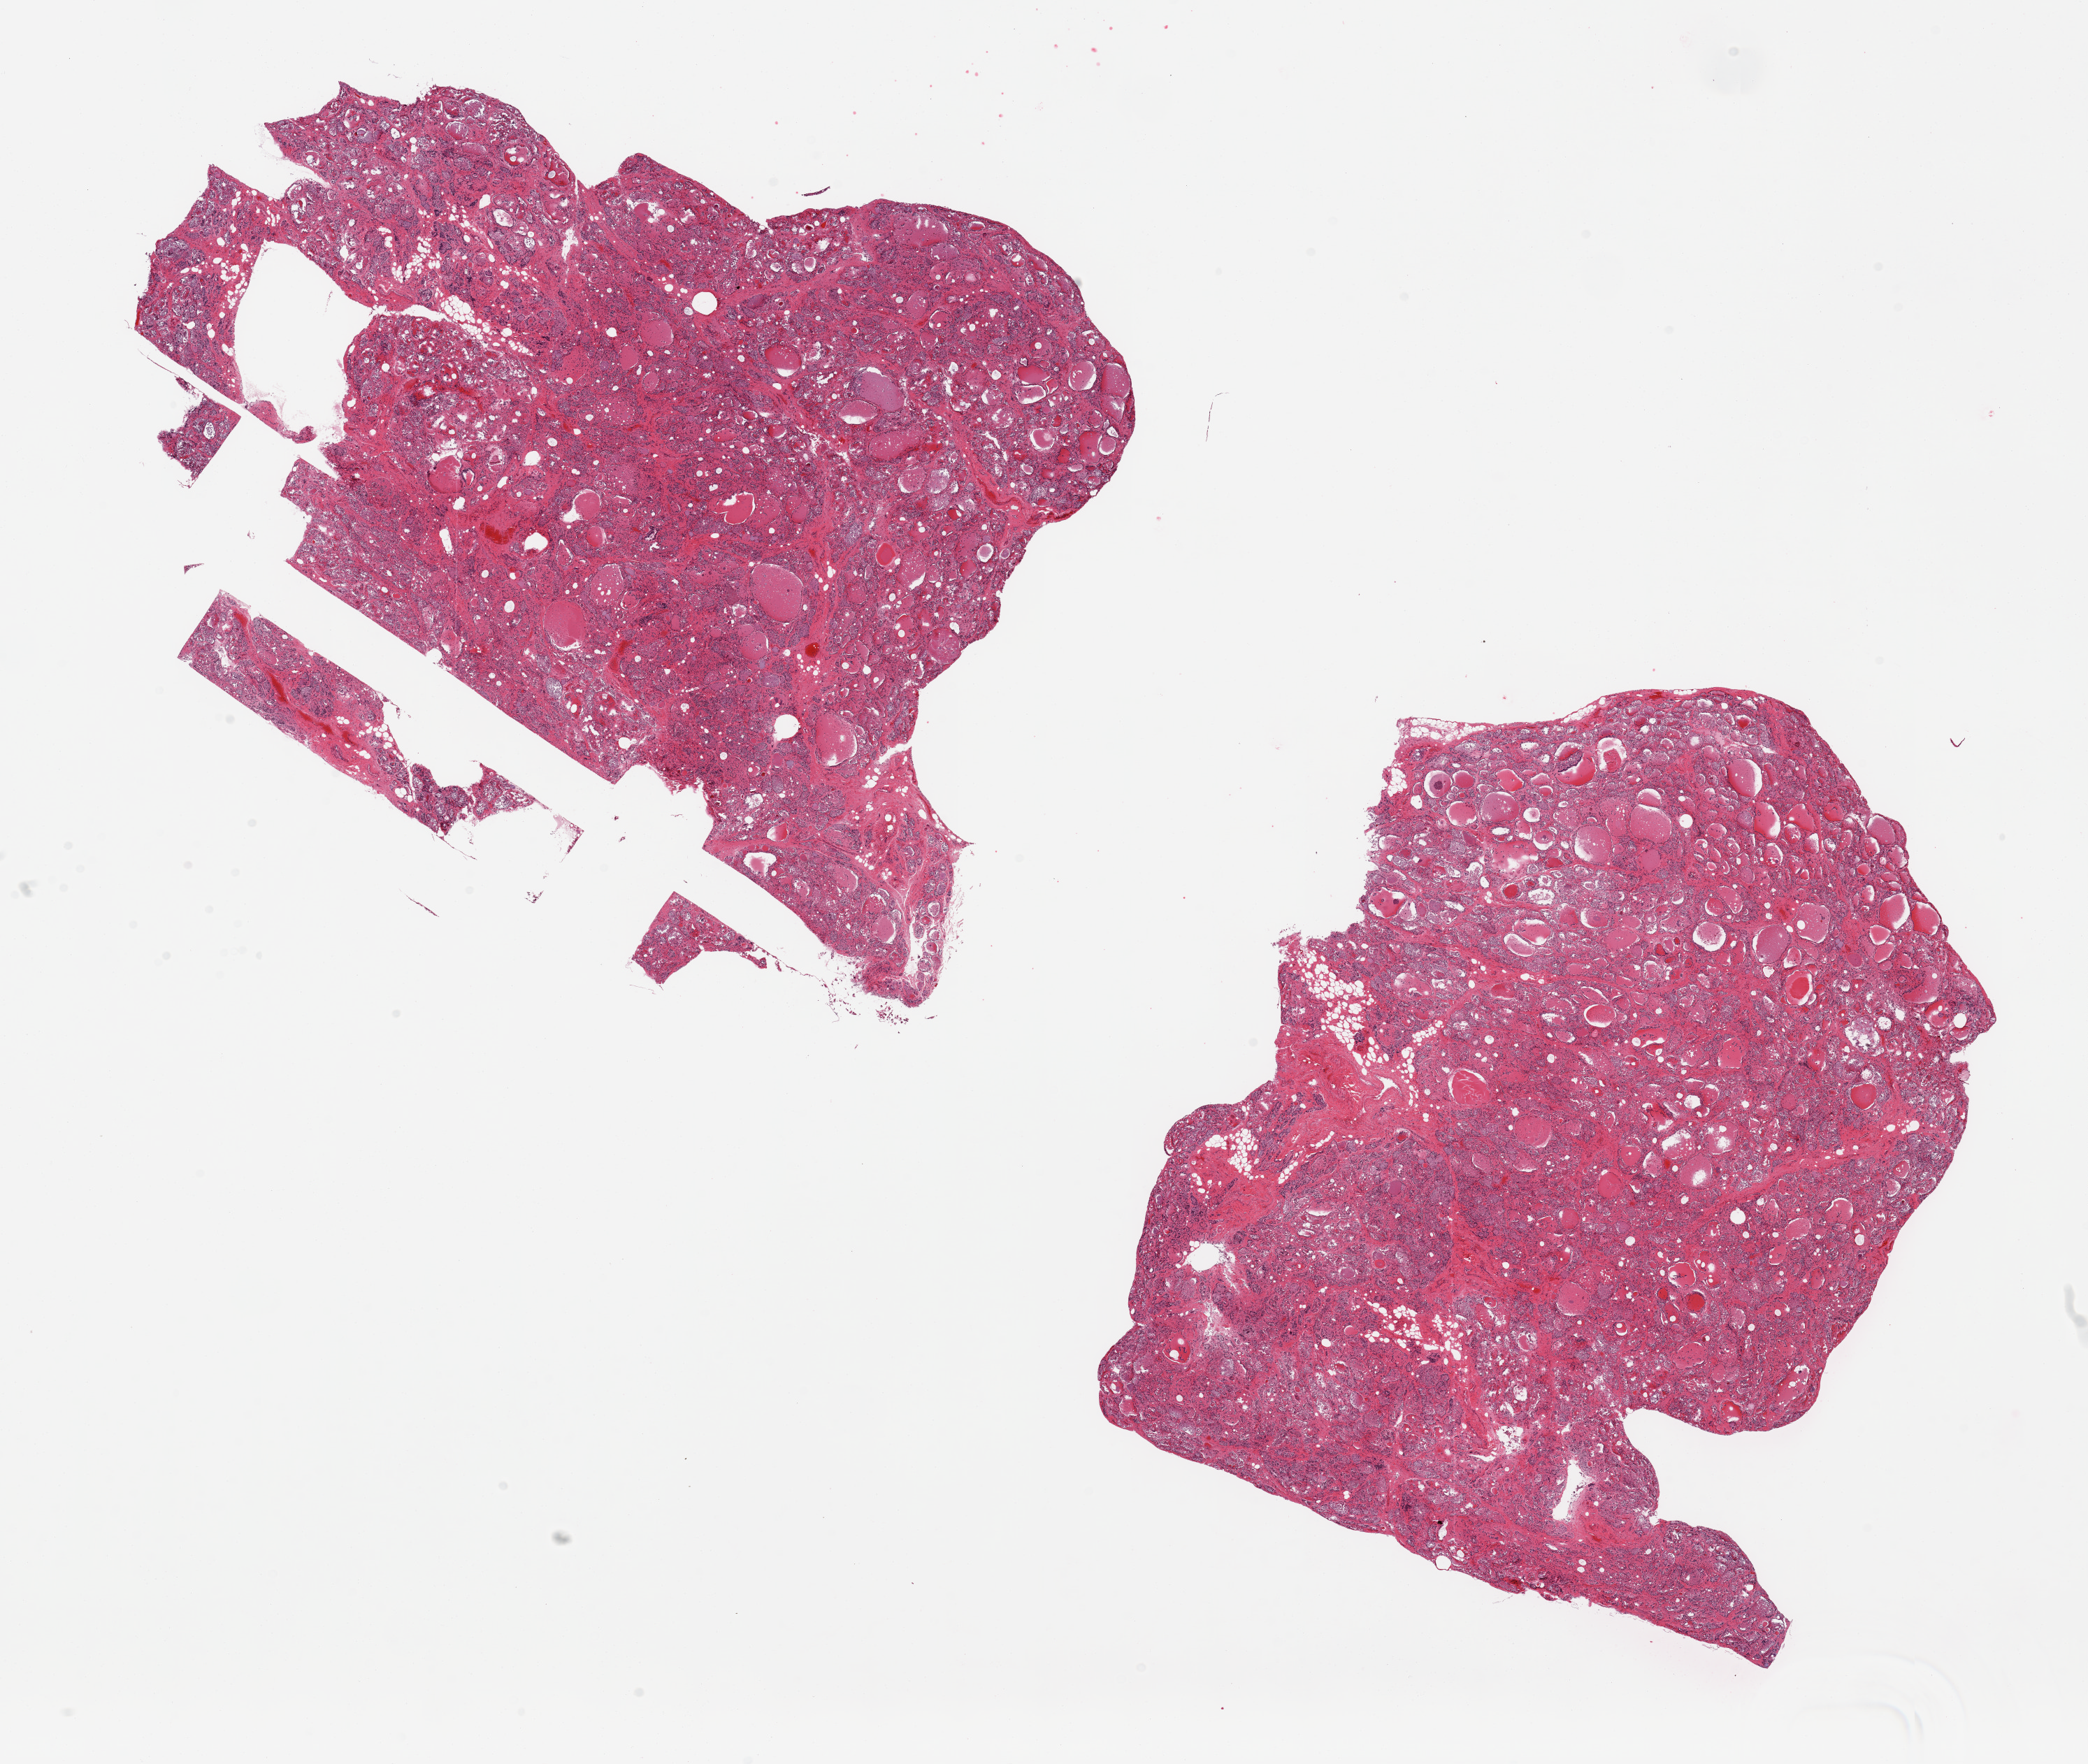
Whole-slide image, haematoxylin and eosin stain, brightfield, a low-resolution overview of the entire scanned area, about 23.6 x 20.0 mm (from a 20x scan). PAXgene-fixed, paraffin-embedded tissue. Sampled site (target tissue): thyroid. Tissue donor sample. Male donor.
Review note (as recorded): 2 pieces.